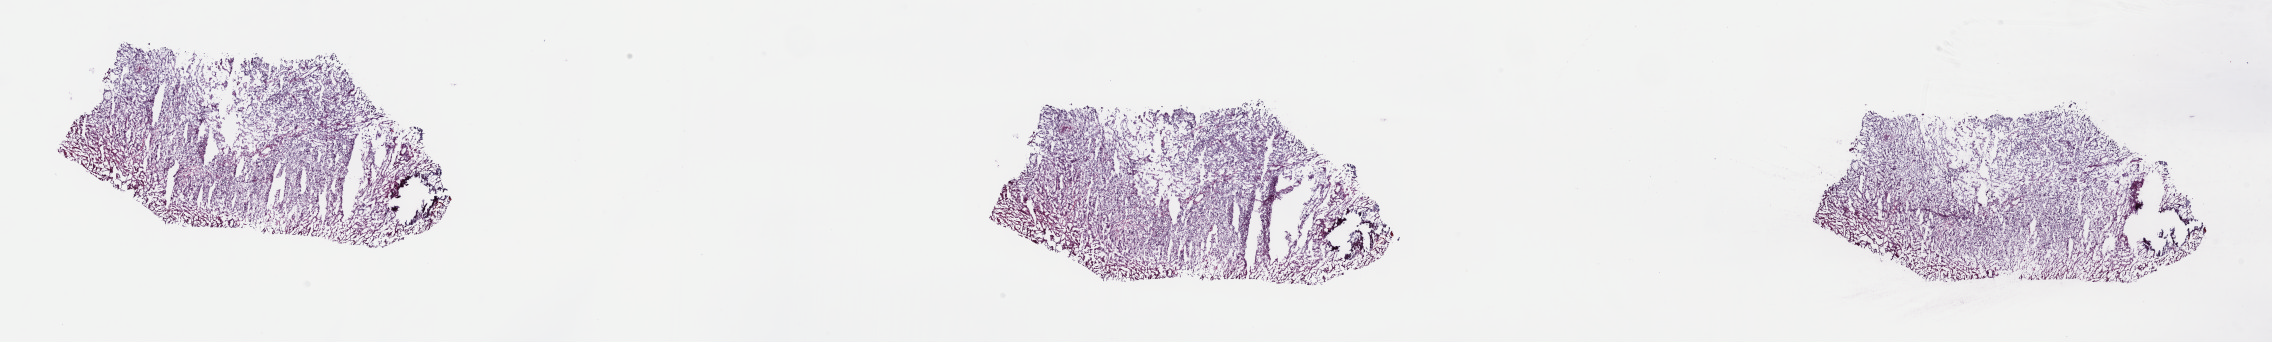
Whole-slide histology image, H&E, shown as a low-resolution overview of the whole scanned area (about 36.7 x 5.5 mm, acquisition: 40x scan); frozen section; sample: primary tumour, bladder. Female, age 53 years at initial diagnosis.
Histologic diagnosis: Transitional cell carcinoma.